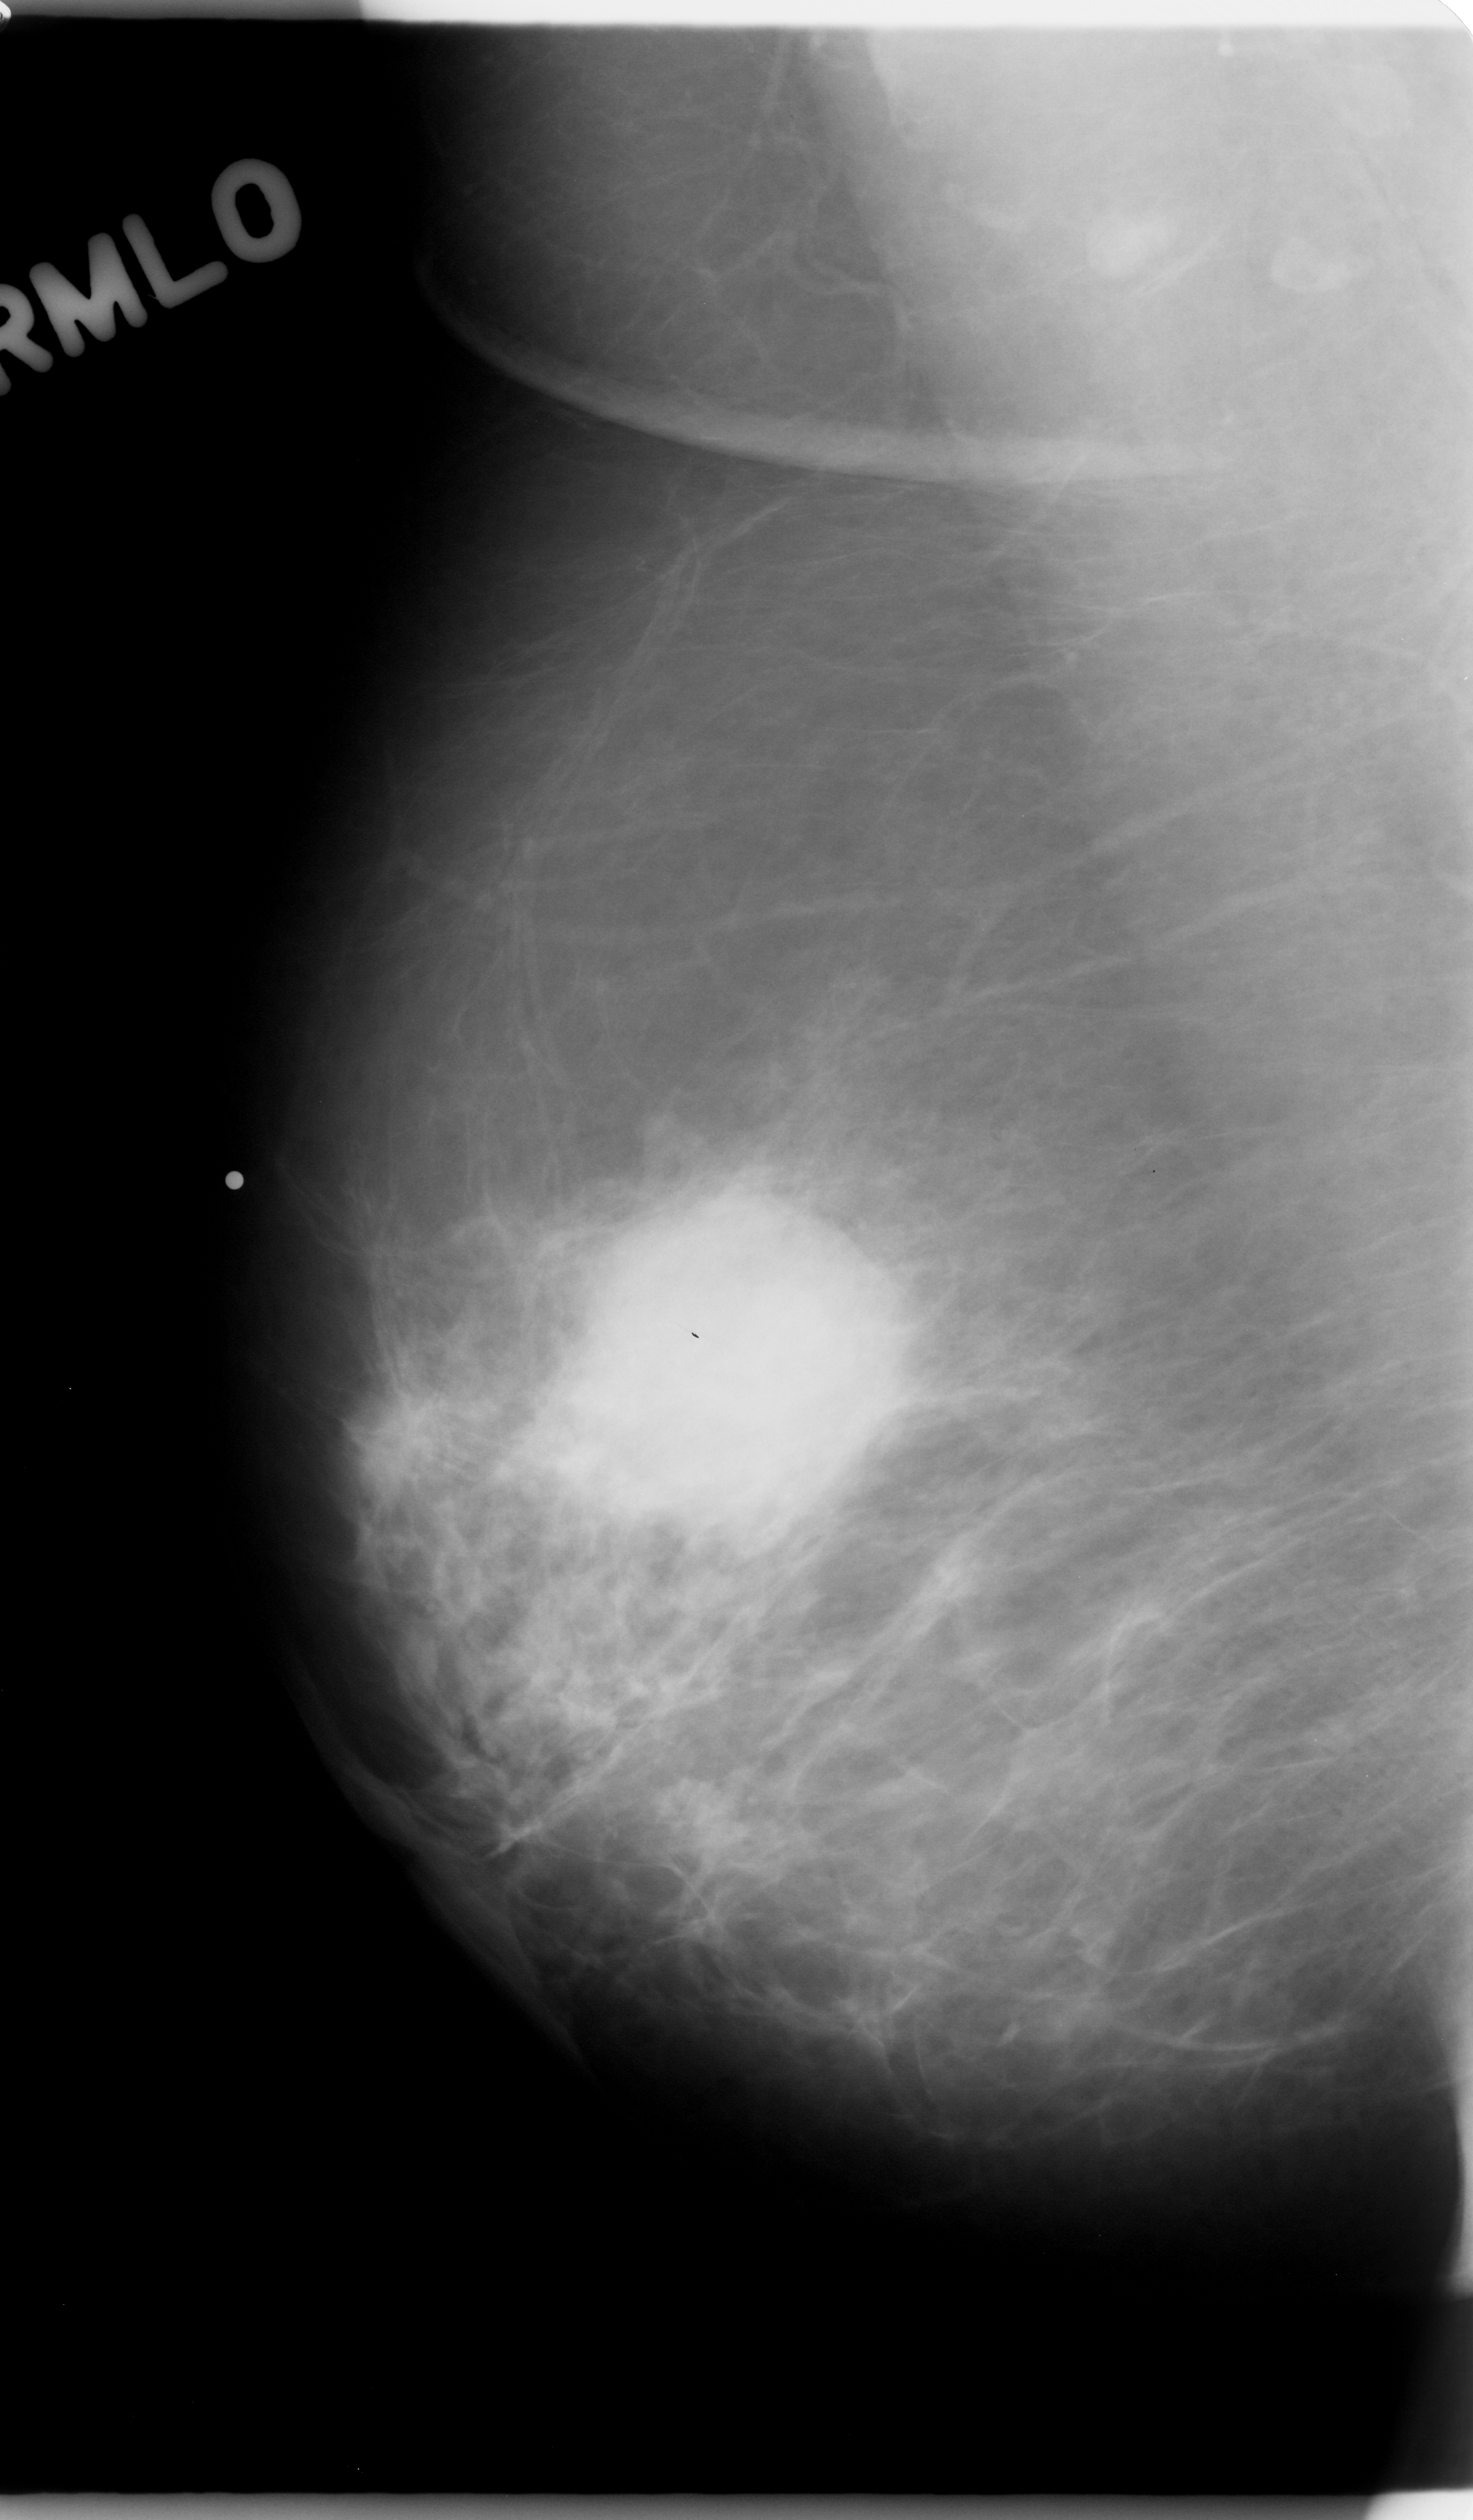
Digitized screen-film mammogram. Right breast. Mediolateral oblique (MLO) view. BI-RADS breast density category 1 (scale 1–4). 1473 × 2520 image matrix.
Expert-marked regions of interest on this film, with their recorded descriptors:
- mass, shape lobulated, margins microlobulated; BI-RADS assessment category 5; subtlety rating 5 on a 1 (subtle) to 5 (obvious) scale; pathology (as recorded): malignant: bounding box <546,1165,895,1560> (left, top, right, bottom; pixels)